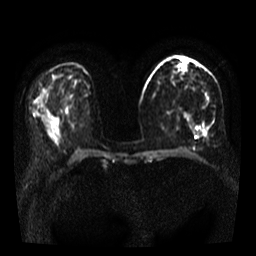
Breast MRI, one axial slice. Slice 18 of 35 in the series (ordered by position). Diffusion-weighted series; image 2 of 4 stored at this slice position (different b-values; order by instance number). 3 T. 5 mm slice thickness. 256 × 256 image matrix, field of view 320 × 320 mm. Female patient.
Annotated regions visible in this slice (manually delineated by an expert):
- tumour on diffusion-weighted imaging: box from (x=195, y=126) to (x=207, y=136) px